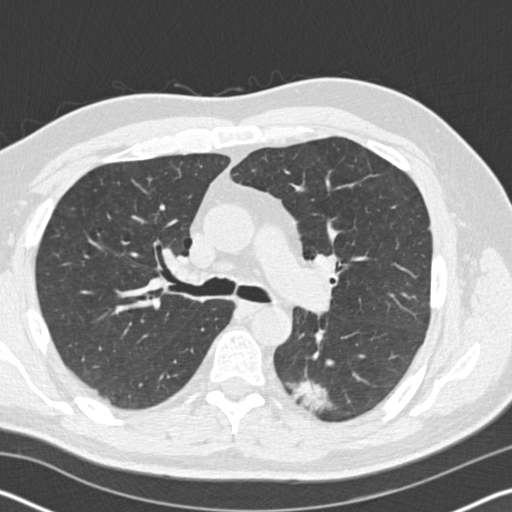
Low-dose screening chest CT, one axial slice. Slice 109 of 178 in the series (ordered by position). Reconstruction kernel B30f. Lung window (W 1500 / L -600 HU). 2 mm slice thickness. 512 × 512 image matrix, field of view 340 × 340 mm.
Annotated regions visible in this slice (expert manual segmentation):
- lesion 1 (tumor, lower lobe of left lung): bounding box [x1, y1, x2, y2] px = [286, 379, 333, 413]